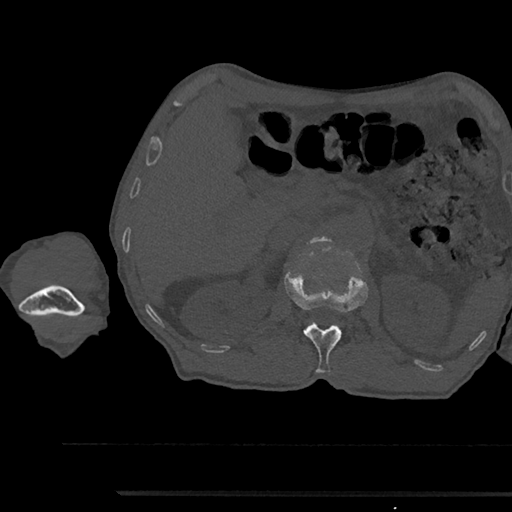
CT including the spine, one axial slice. Slice 624 of 797 in the series (ordered by position). Reconstruction kernel Br40s/3. Bone window (W 1800 / L 400 HU). 0.5 mm slice thickness. 512 × 512 image matrix, field of view 367 × 367 mm. Male patient, age 79 years. From the clinical record (not read from this slice): primary cancer: prostate.
Annotated regions visible in this slice (semi-automatic segmentation, software-assisted and operator-edited):
- L1 vertebra: bounding box <285,272,368,373> (left, top, right, bottom; pixels)
- L2 vertebra: <308,236,328,243>